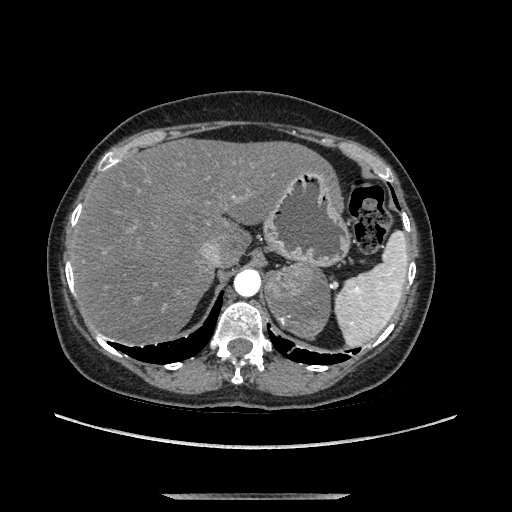
Contrast-enhanced abdominal CT, one axial slice. Position 102 of 169 along the scan axis. Soft-tissue window (W 400 / L 40 HU). 512 × 512 image matrix, field of view 400 × 400 mm. Female patient. Case-level facts recorded for this patient, not image findings: diagnosis: adrenocortical carcinoma; tumour side: left adrenal; tumour size at pathology: 9 cm; Ki-67 index: 2 %; stage (as recorded): 3.
Outlined on this slice (semi-automatically segmented with operator editing):
- mass: box from (x=266, y=263) to (x=330, y=334) px